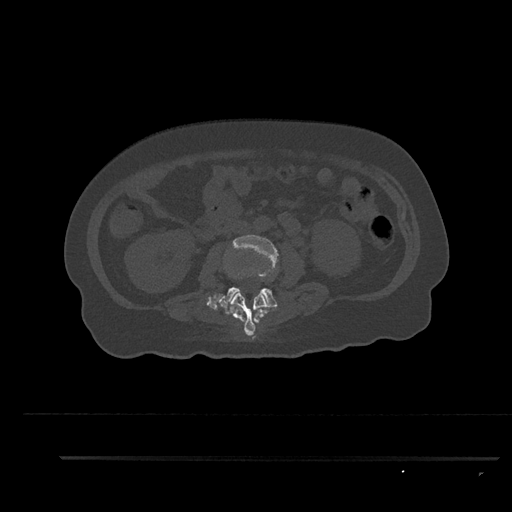
CT including the spine, one axial slice. Position 120 of 797 along the scan axis. Reconstruction kernel Br40s/3. 120 kVp. Bone window (W 1800 / L 400 HU). 0.5 mm slice thickness. 512 × 512 image matrix, field of view 408 × 408 mm. Female patient, age 44 years. Case-level facts recorded for this patient, not image findings: primary cancer: renal; vertebrae with lytic lesions (as recorded): L1.
Outlined on this slice (semi-automatically segmented with operator editing):
- L2 vertebra: bounding box [x1, y1, x2, y2] px = [225, 292, 269, 336]
- L3 vertebra: [220, 235, 279, 308]